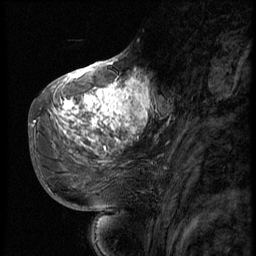
Breast MRI (dynamic contrast-enhanced), one sagittal slice; position 27 of 56 along the scan axis; 3 images stored at this slice position (order not interpretable as contrast timing); 1.5 T; TE 4.2 ms, TR 9 ms; 2.5 mm slice thickness; 256 × 256 image matrix, field of view 180 × 180 mm. Female patient, age 51 years. From the clinical record (not read from this slice): setting: breast cancer imaged before/during neoadjuvant chemotherapy; receptor status: triple-negative.
Annotated regions visible in this slice (semi-automatically segmented with operator editing):
- analysis volume of interest (the breast-tissue region the enhancement analysis was run in; not a lesion): box from (x=52, y=66) to (x=156, y=179) px
- tumour enhancement mask (voxels above the 140 % enhancement threshold inside the analysis volume of interest): (x=54, y=72)–(x=150, y=149)